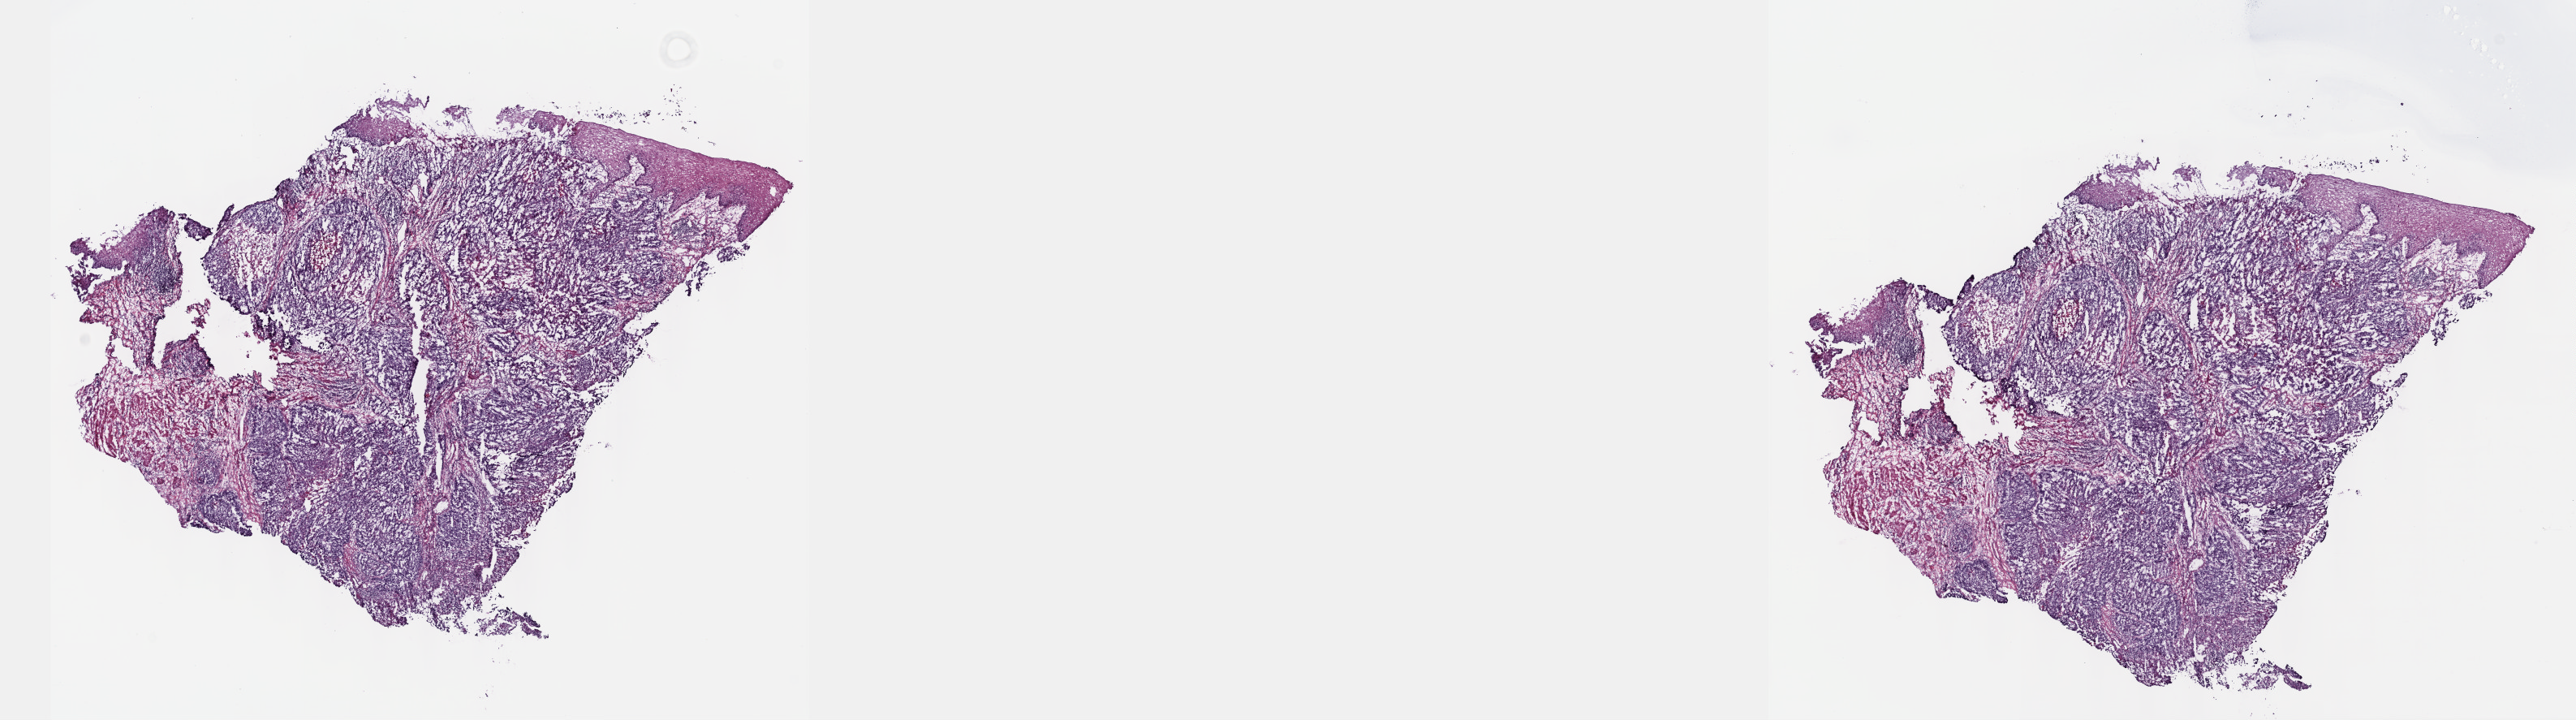
Digitized H&E tissue section (whole slide) — shown as a low-resolution overview of the whole scanned area (about 25.7 x 7.2 mm, slide scanned at 40x), frozen section from the top of the tissue portion, esophagus, primary tumour sample. Patient: male, age at initial diagnosis 51 years.
Diagnosis: Squamous cell carcinoma, NOS (middle third of esophagus).